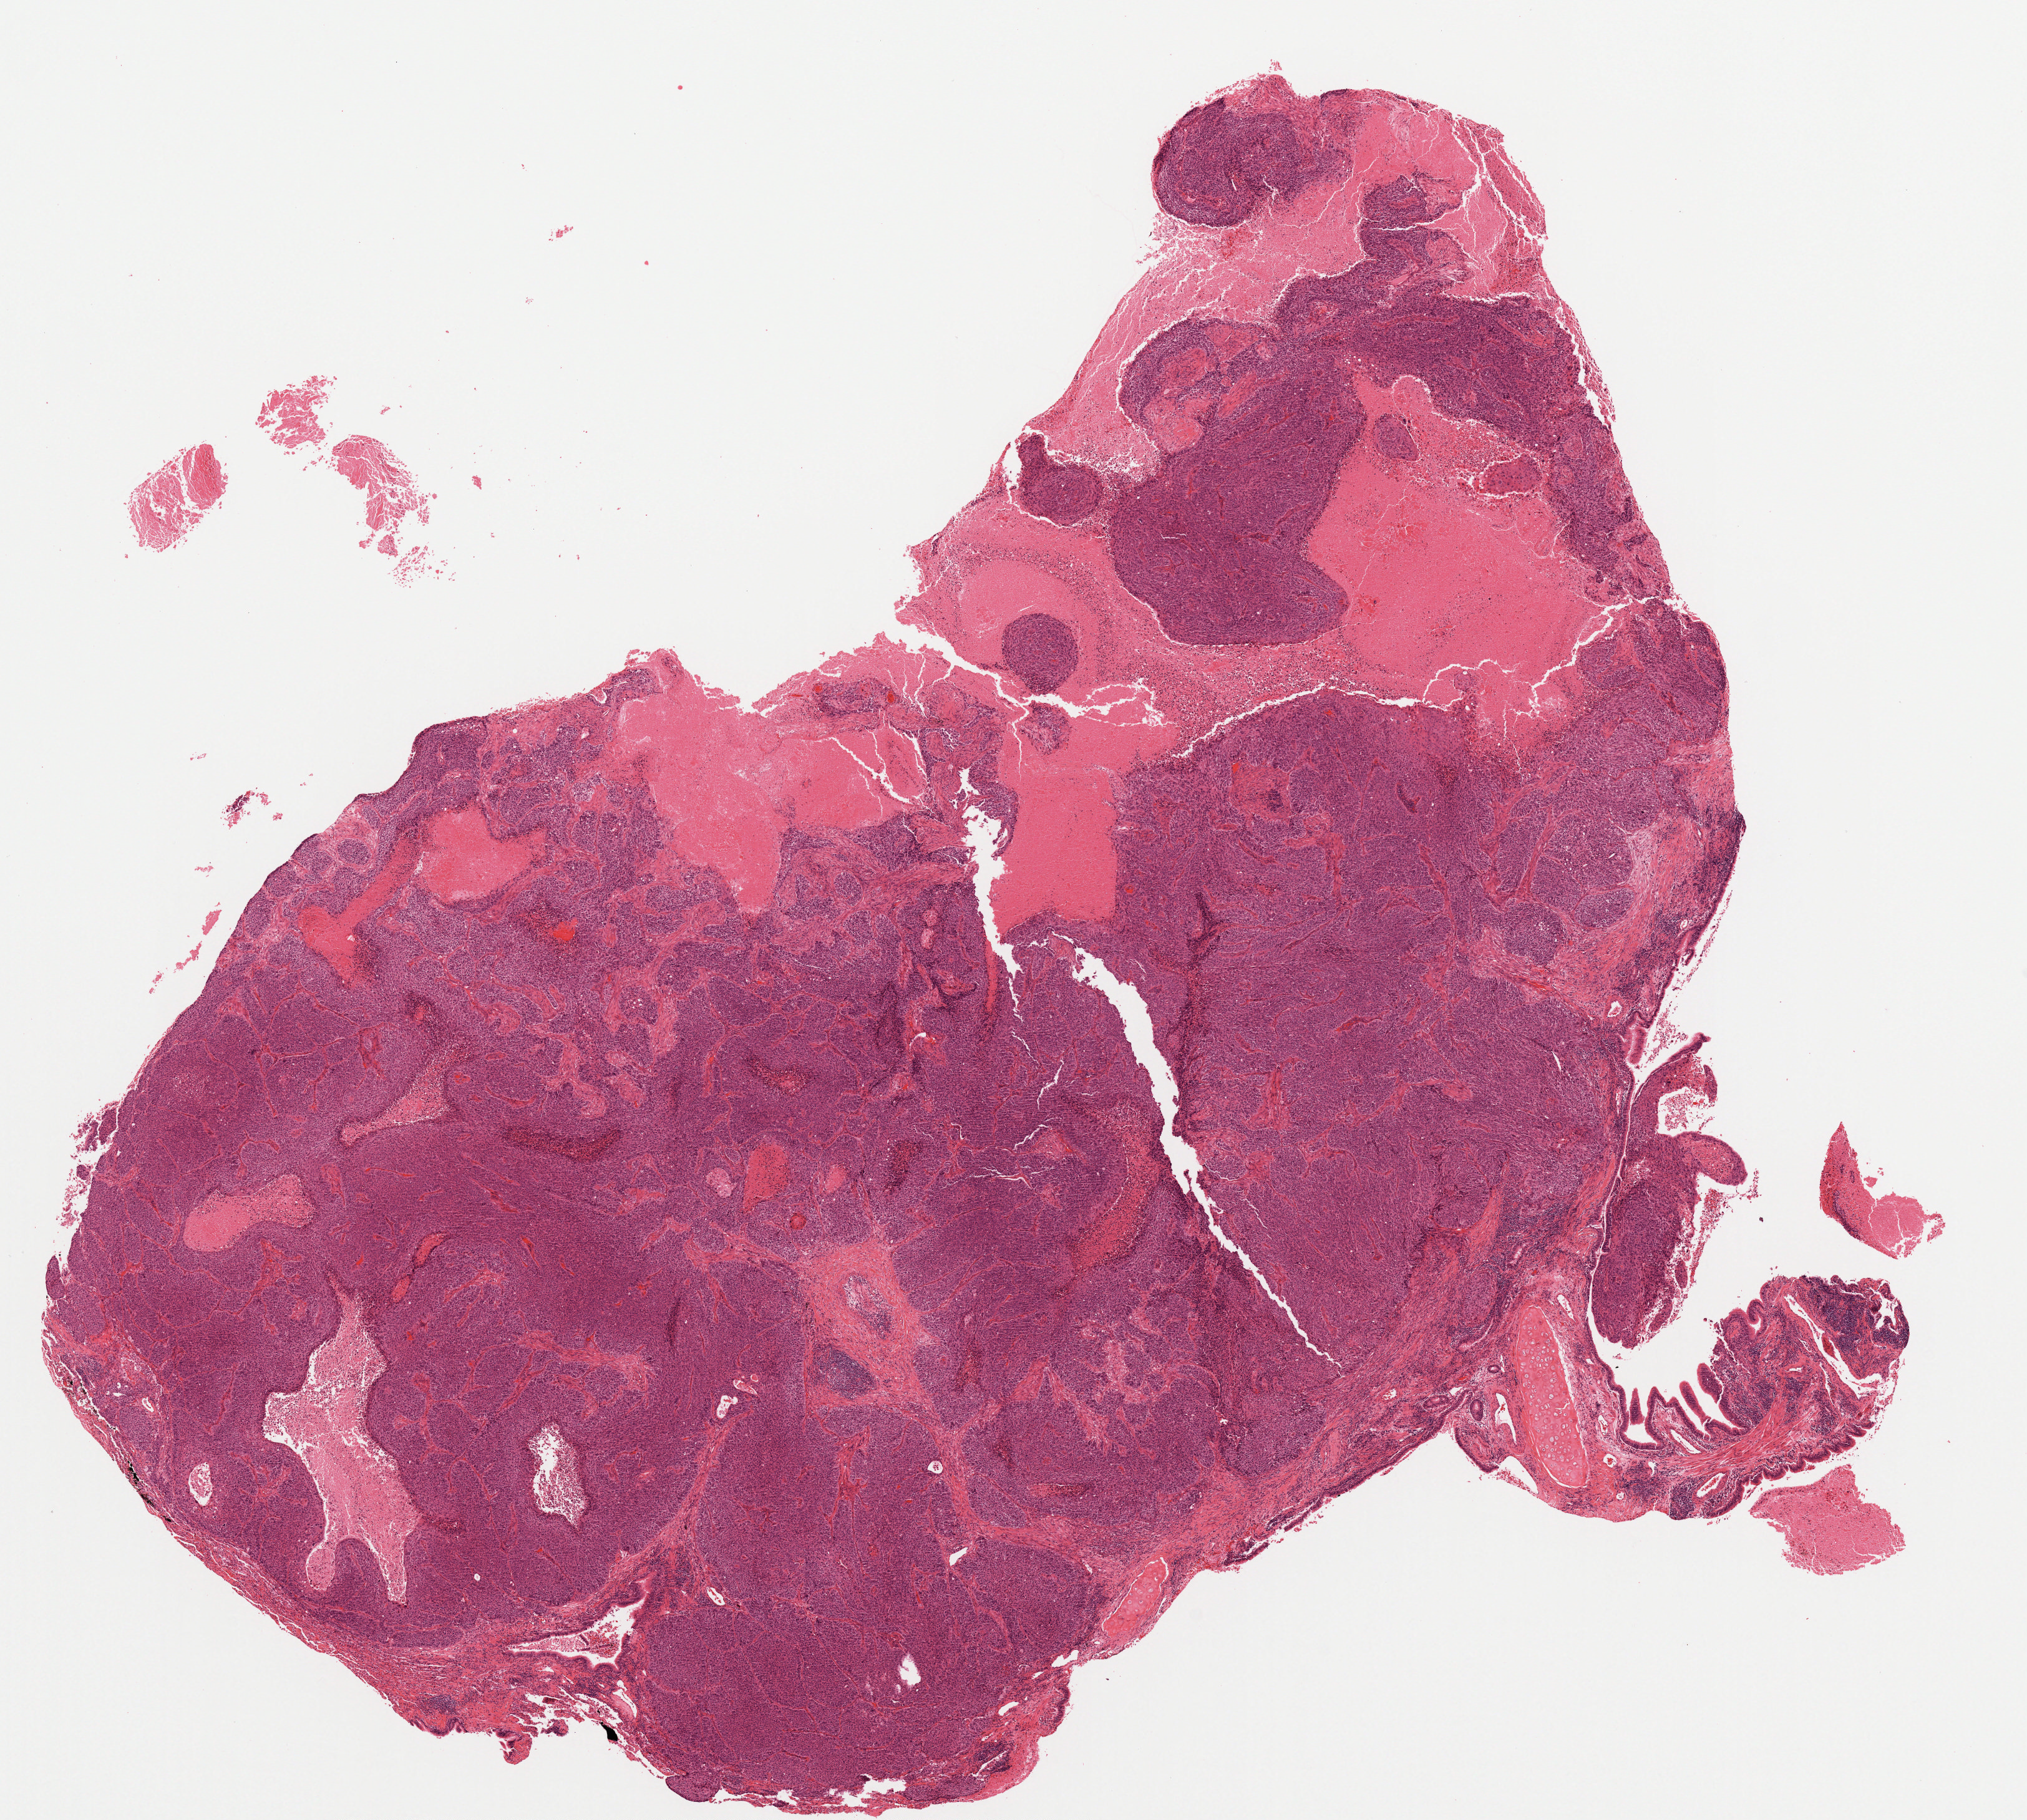
Hematoxylin and eosin (H&E) stained whole-slide image, whole scanned area (about 13.0 x 11.7 mm, acquisition: 20x scan) shown as a low-resolution overview; formalin-fixed paraffin-embedded (FFPE) diagnostic section; lung, primary tumour sample. Male patient; age at initial diagnosis 68 years.
* pathologic diagnosis: Squamous cell carcinoma, NOS (lower lobe, lung)
* AJCC pathologic stage: IB (6th edition)